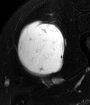
MRI of an extremity soft-tissue mass, one axial slice; position 35 of 65 along the scan axis; T2-weighted fat-saturated; MR volume resampled by the dataset authors to the PET/CT grid (not the native acquisition matrix); 3.27 mm slice thickness; 90 × 105 image matrix. Male patient. Case-level facts recorded for this patient, not image findings: histological type: mixoid liposarcoma; grade: low; site of the primary tumour: left thigh.
Outlined on this slice (expert contour drawn on MRI and transferred to this co-registered scan by the dataset authors):
- gross tumour volume (mass): bounding box [x1, y1, x2, y2] px = [16, 21, 65, 76]